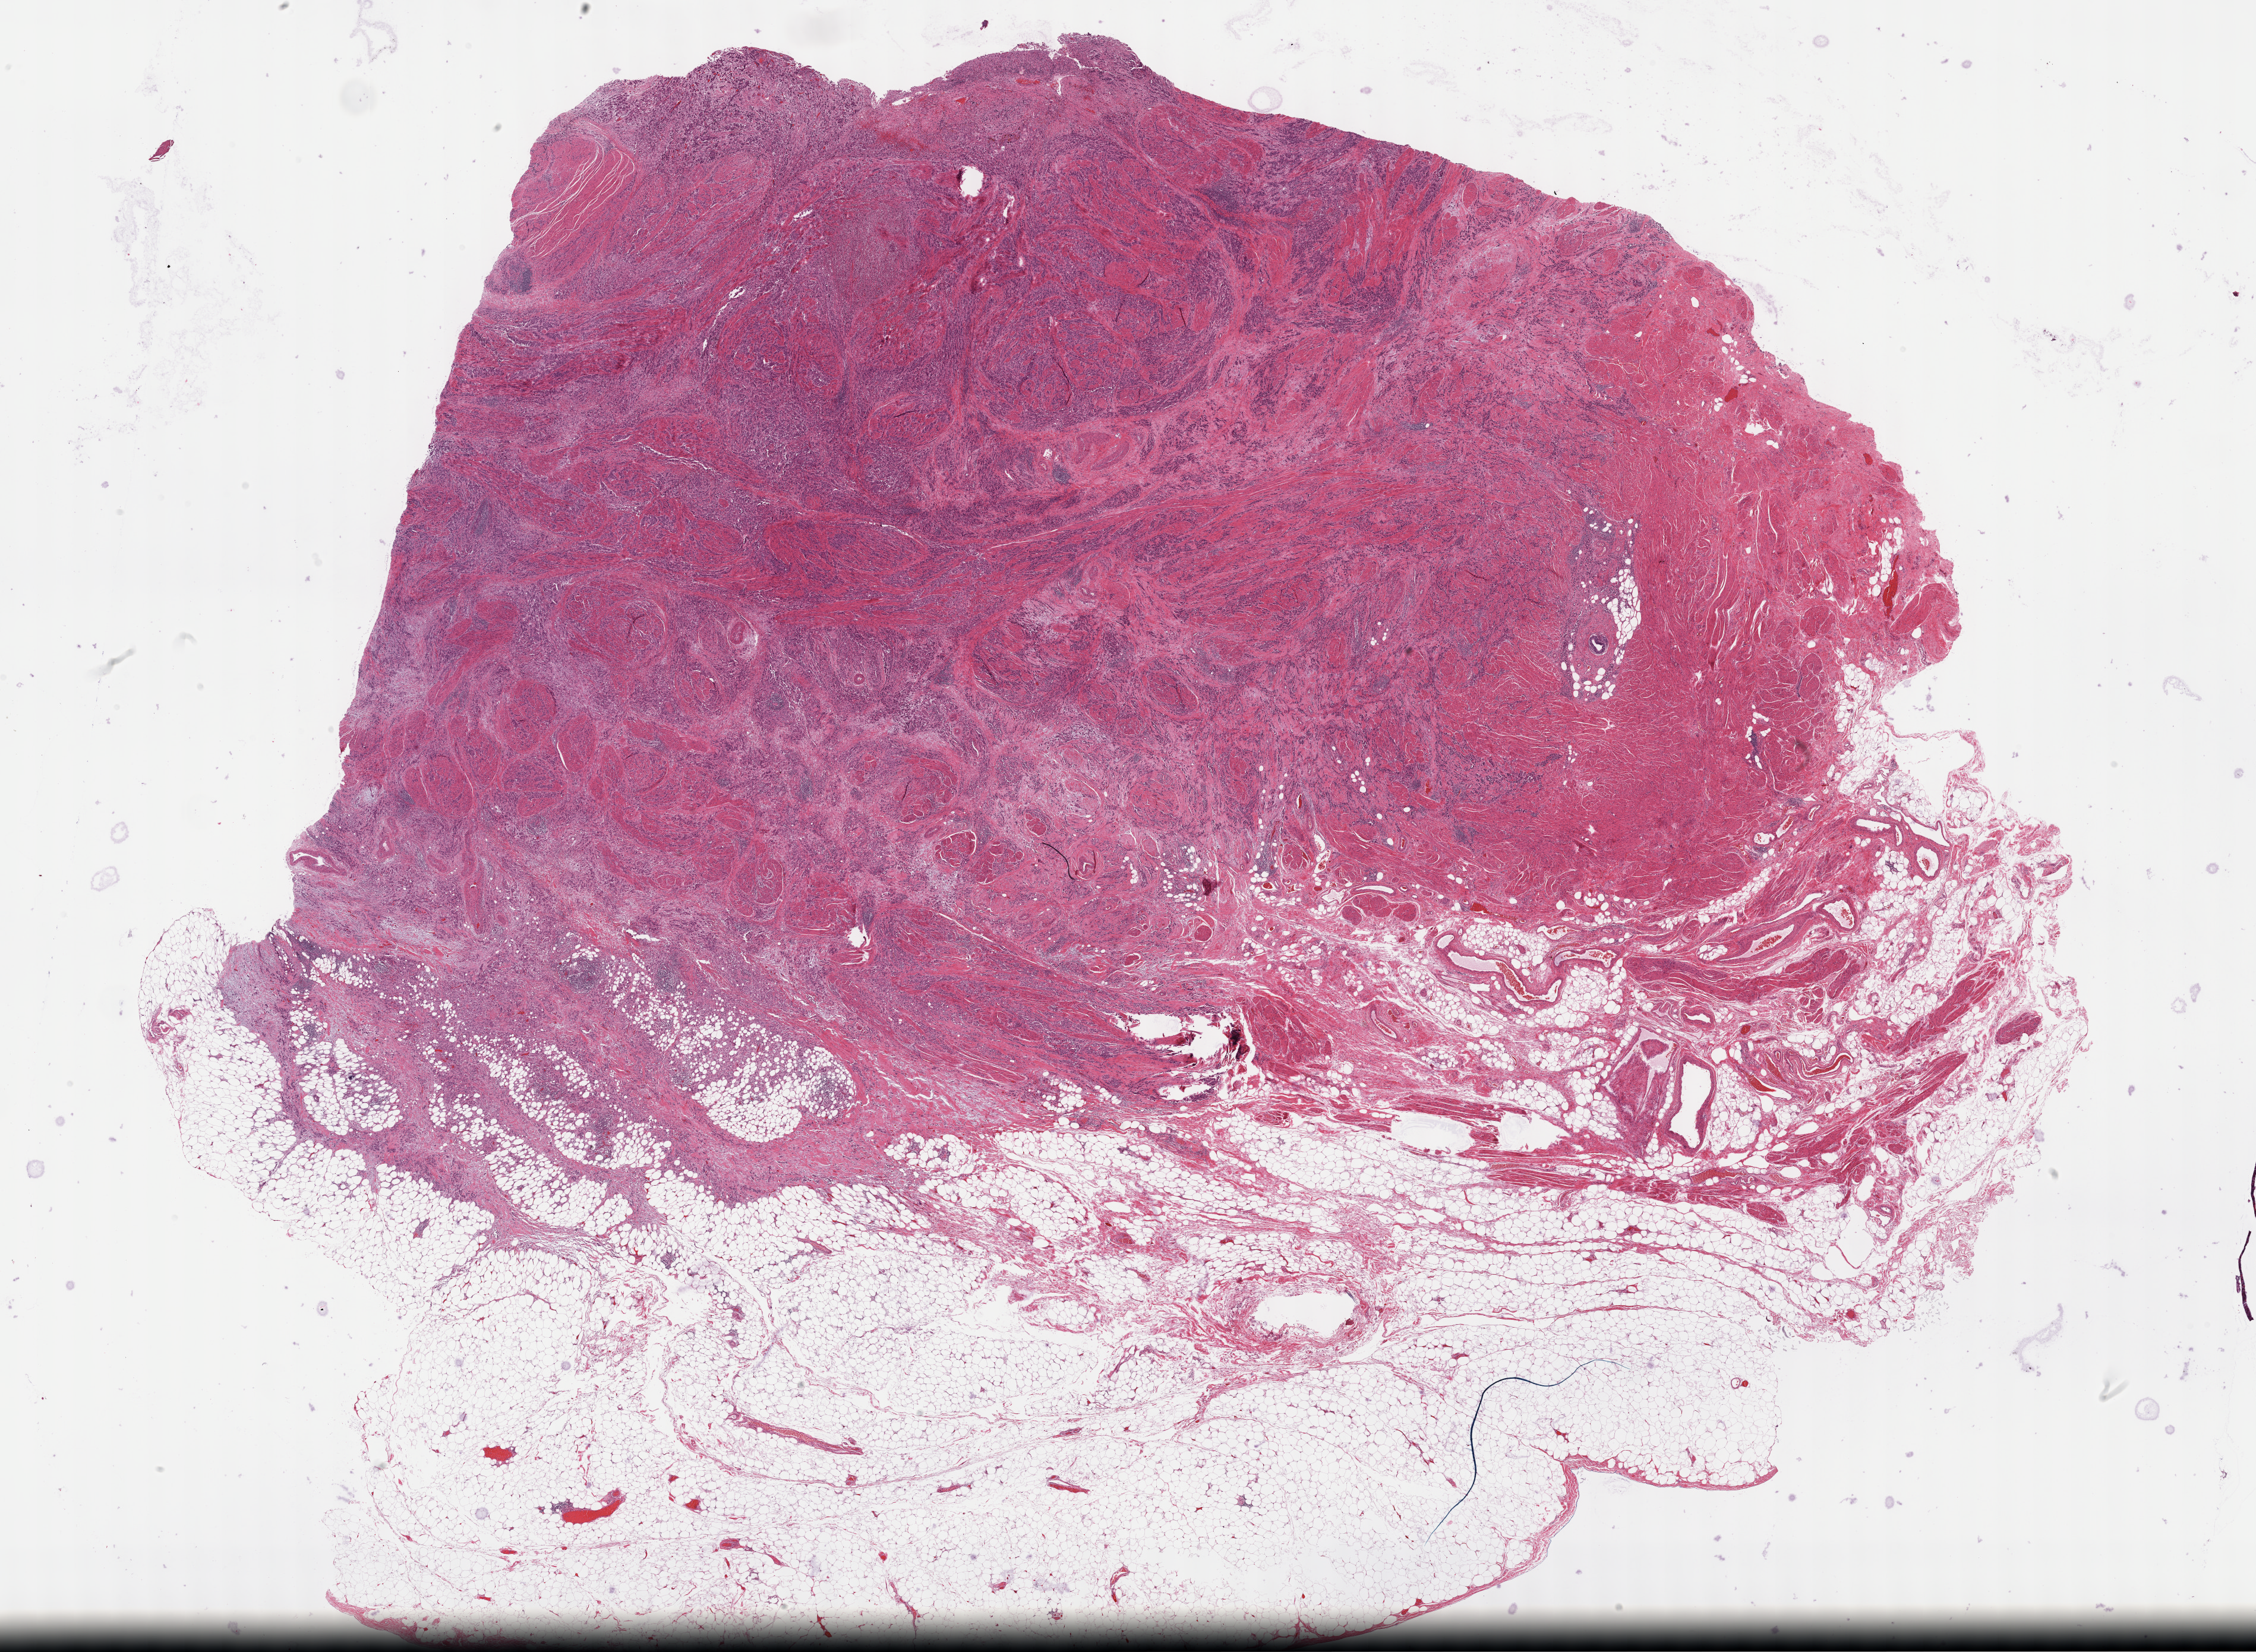
H&E whole-slide image — shown as a low-resolution overview of the whole scanned area (about 30.7 x 22.5 mm, from a 40x scan), formalin-fixed paraffin-embedded (FFPE) diagnostic section, bladder, primary tumour sample. Male patient; age at initial diagnosis 73 years. Histologic grade: high grade.
Diagnosis: Transitional cell carcinoma (lateral wall of bladder). AJCC pathologic stage: IV (7th edition). Lymph nodes positive (case pathology): 3 of 14 examined.